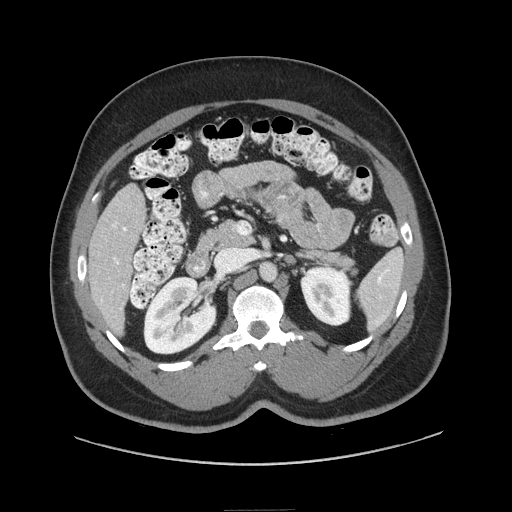
Contrast-enhanced abdominal CT (liver protocol), one axial slice. Position 29 of 87 along the scan axis. Reconstruction kernel STANDARD. Soft-tissue window (W 400 / L 40 HU). 512 × 512 image matrix, field of view 440 × 440 mm. Case-level facts recorded for this patient, not image findings: diagnosis: hepatocellular carcinoma (patient treated with transarterial chemoembolisation; whether this scan precedes or follows treatment is not stated here); TNM stage (as recorded): Stage-II.
Outlined on this slice (semi-automatically segmented with operator editing):
- liver parenchyma outside the tumour (the mass and vessels are separate outlines, so this box may not span the whole liver): bounding box <87,184,146,332> (left, top, right, bottom; pixels)
- liver vessels: <101,221,127,302>